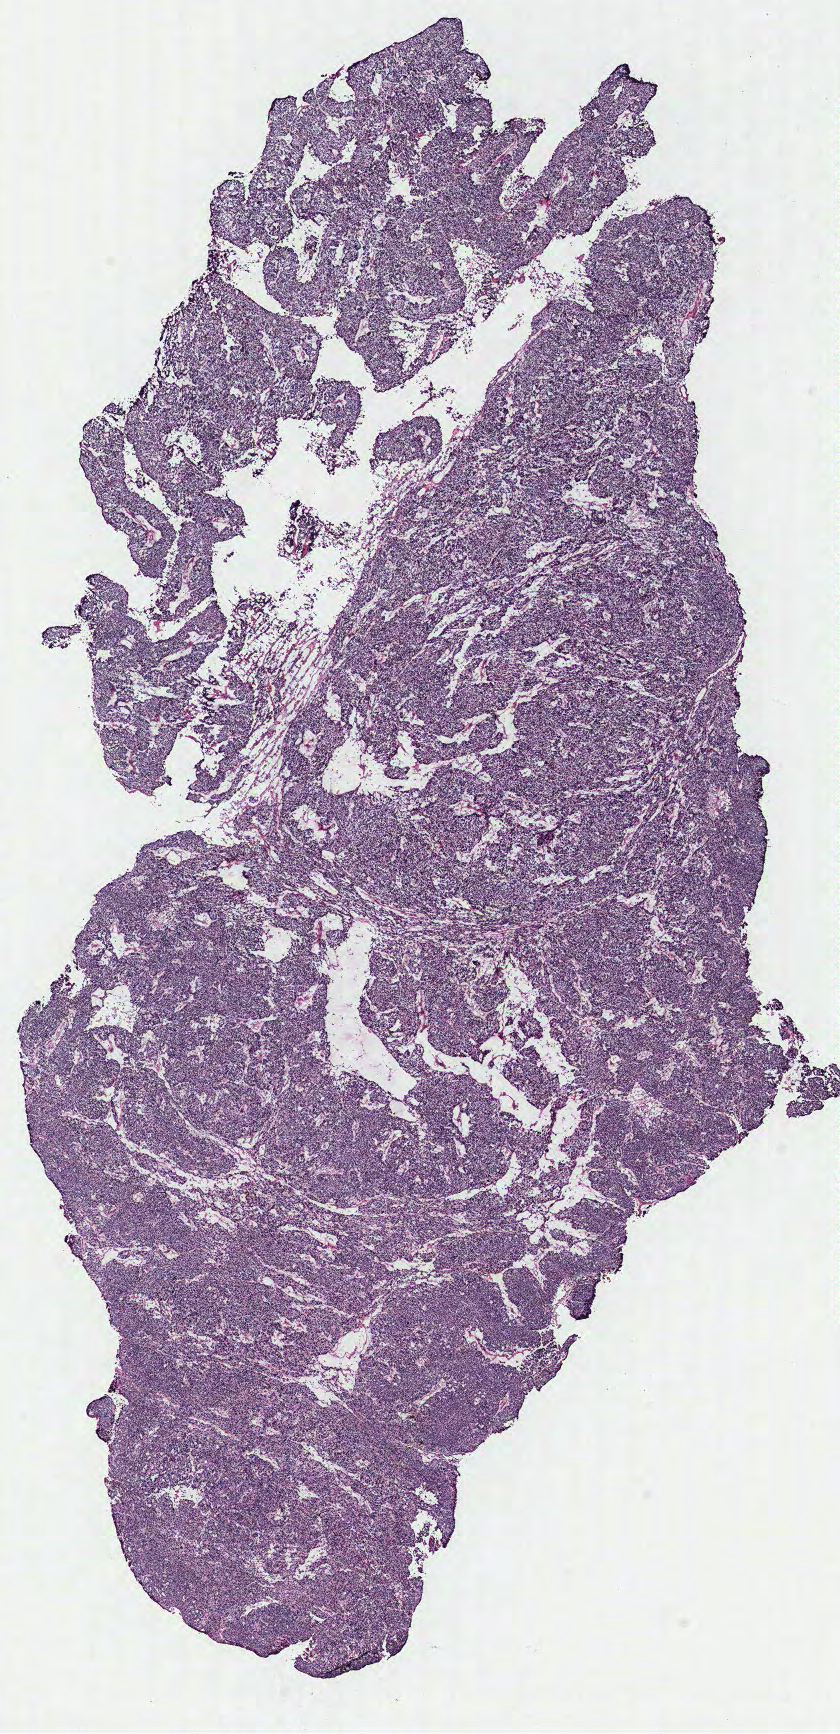
Whole-slide histology image, H&E — whole scanned area (about 6.7 x 13.9 mm, slide scanned at 40x) shown as a low-resolution overview. Ovary, tumour tissue. Female, 51 y/o.
Diagnosis: Serous adenocarcinoma, NOS. Primary tumour site (as recorded): ovary.